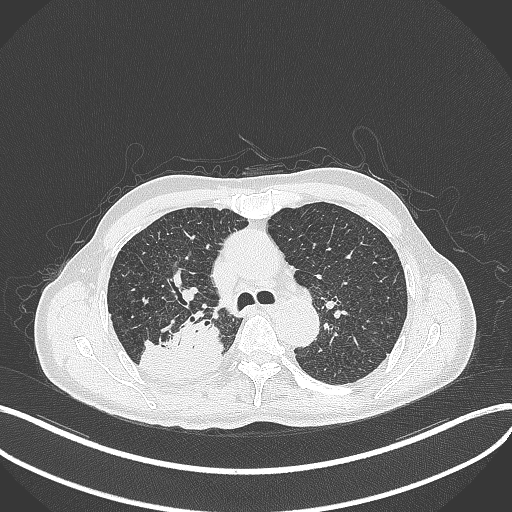
Chest CT, one axial slice; position 307 of 428 along the scan axis; lung window (W 1500 / L -600 HU); 512 × 512 image matrix. Male patient, age 79 years. Case-level facts recorded for this patient, not image findings: clinical TNM (as recorded): T3 N0 M0.
Structures marked on this image (rectangle marked by the reading radiologist):
- lung tumour (recorded histology: adenocarcinoma): bounding box <139,311,226,383> (left, top, right, bottom; pixels)